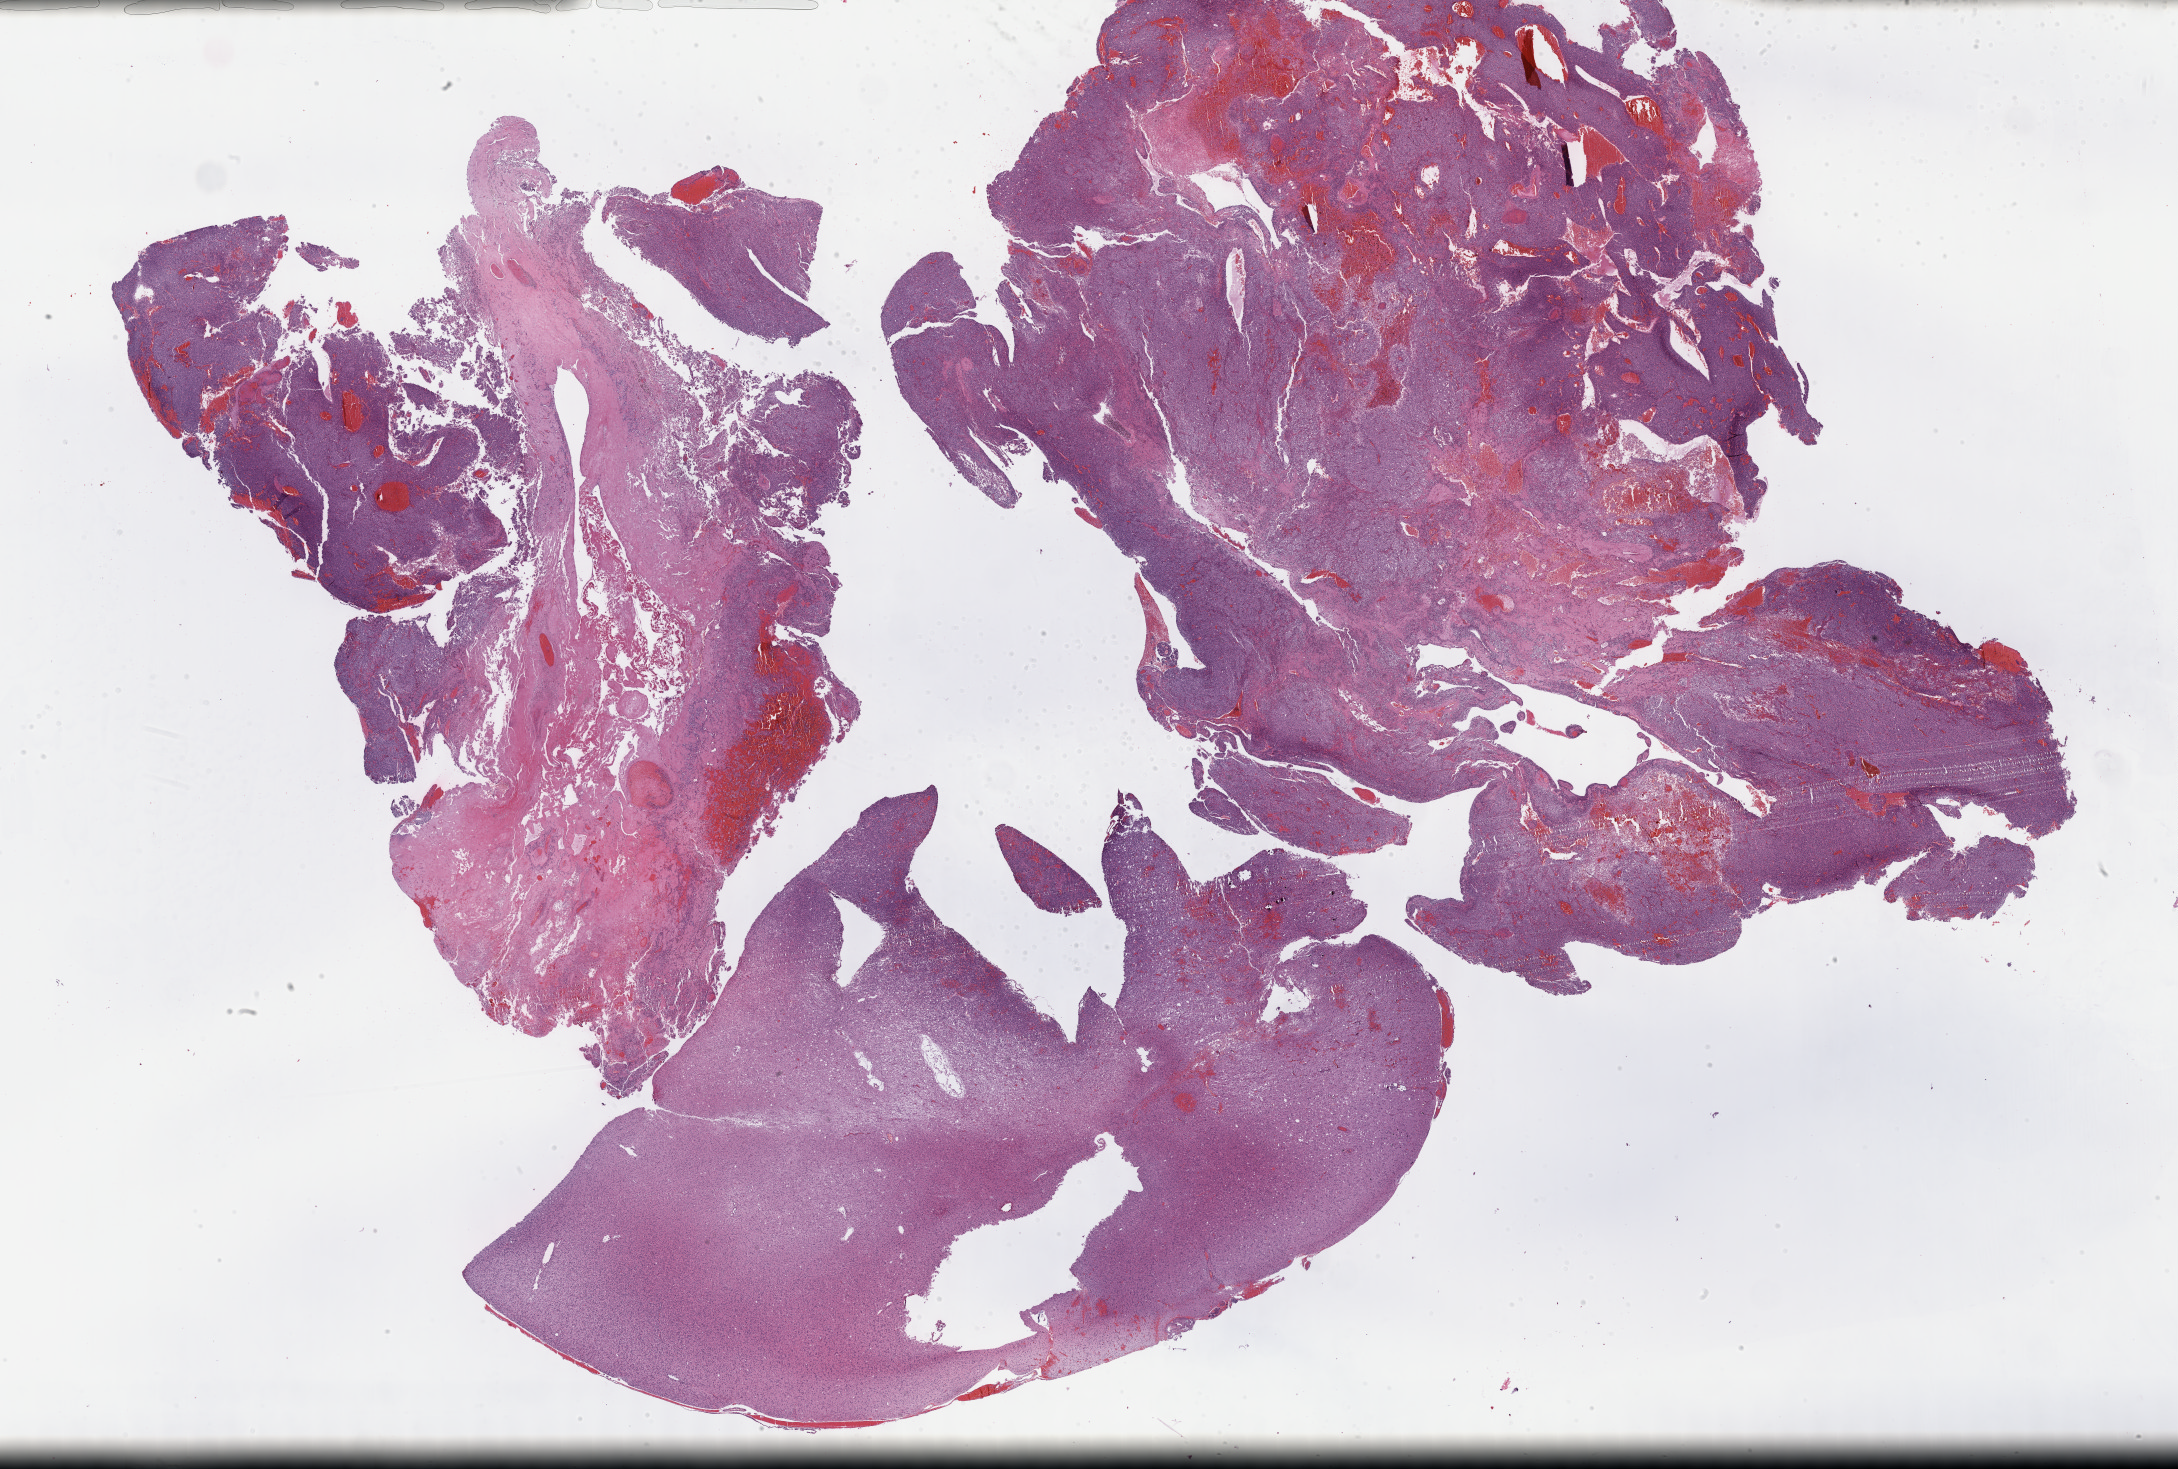
Whole-slide histology image, H&E, whole scanned area (about 35.2 x 23.8 mm, acquisition: 40x scan) shown as a low-resolution overview, FFPE section, primary tumour sample from the brain. Male, age 33 years at initial diagnosis. Histologic grade: G3 (poorly differentiated).
Histologic diagnosis: Oligodendroglioma, anaplastic.